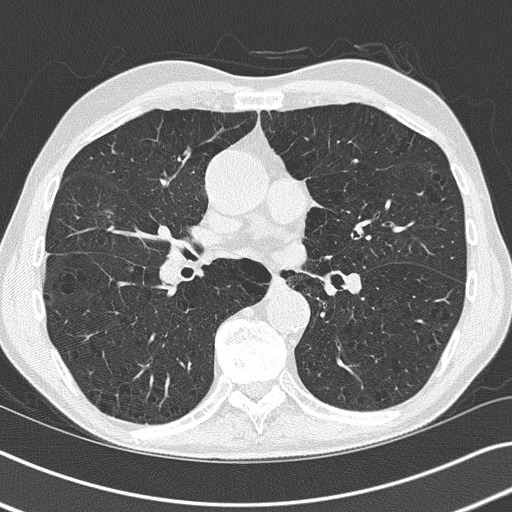
Chest CT (low-dose screening protocol), one axial image; first (baseline) screen; lung window (W 1500 / L -600 HU); 2 mm slice thickness; lung (sharp) reconstruction kernel (B50f). Male, age 73 years at enrolment. Current smoker at enrolment.
Expert-annotated lung lesion, box from (x=85, y=187) to (x=135, y=232) px. The screening reader recorded 3 non-calcified nodules or masses ≥4 mm on this exam (right upper lobe, right middle lobe, right upper lobe); which of them this box marks is not recorded. Official screen result: positive, change unspecified: nodule(s) >= 4 mm or enlarging nodule(s), mass(es), or other non-specific abnormalities suspicious for lung cancer. Later outcome: lung cancer diagnosed 45 days after this screen — bronchiolo-alveolar adenocarcinoma, NOS, right middle lobe, well differentiated (G1), stage IA (AJCC 6th edition), 11 mm at pathology.